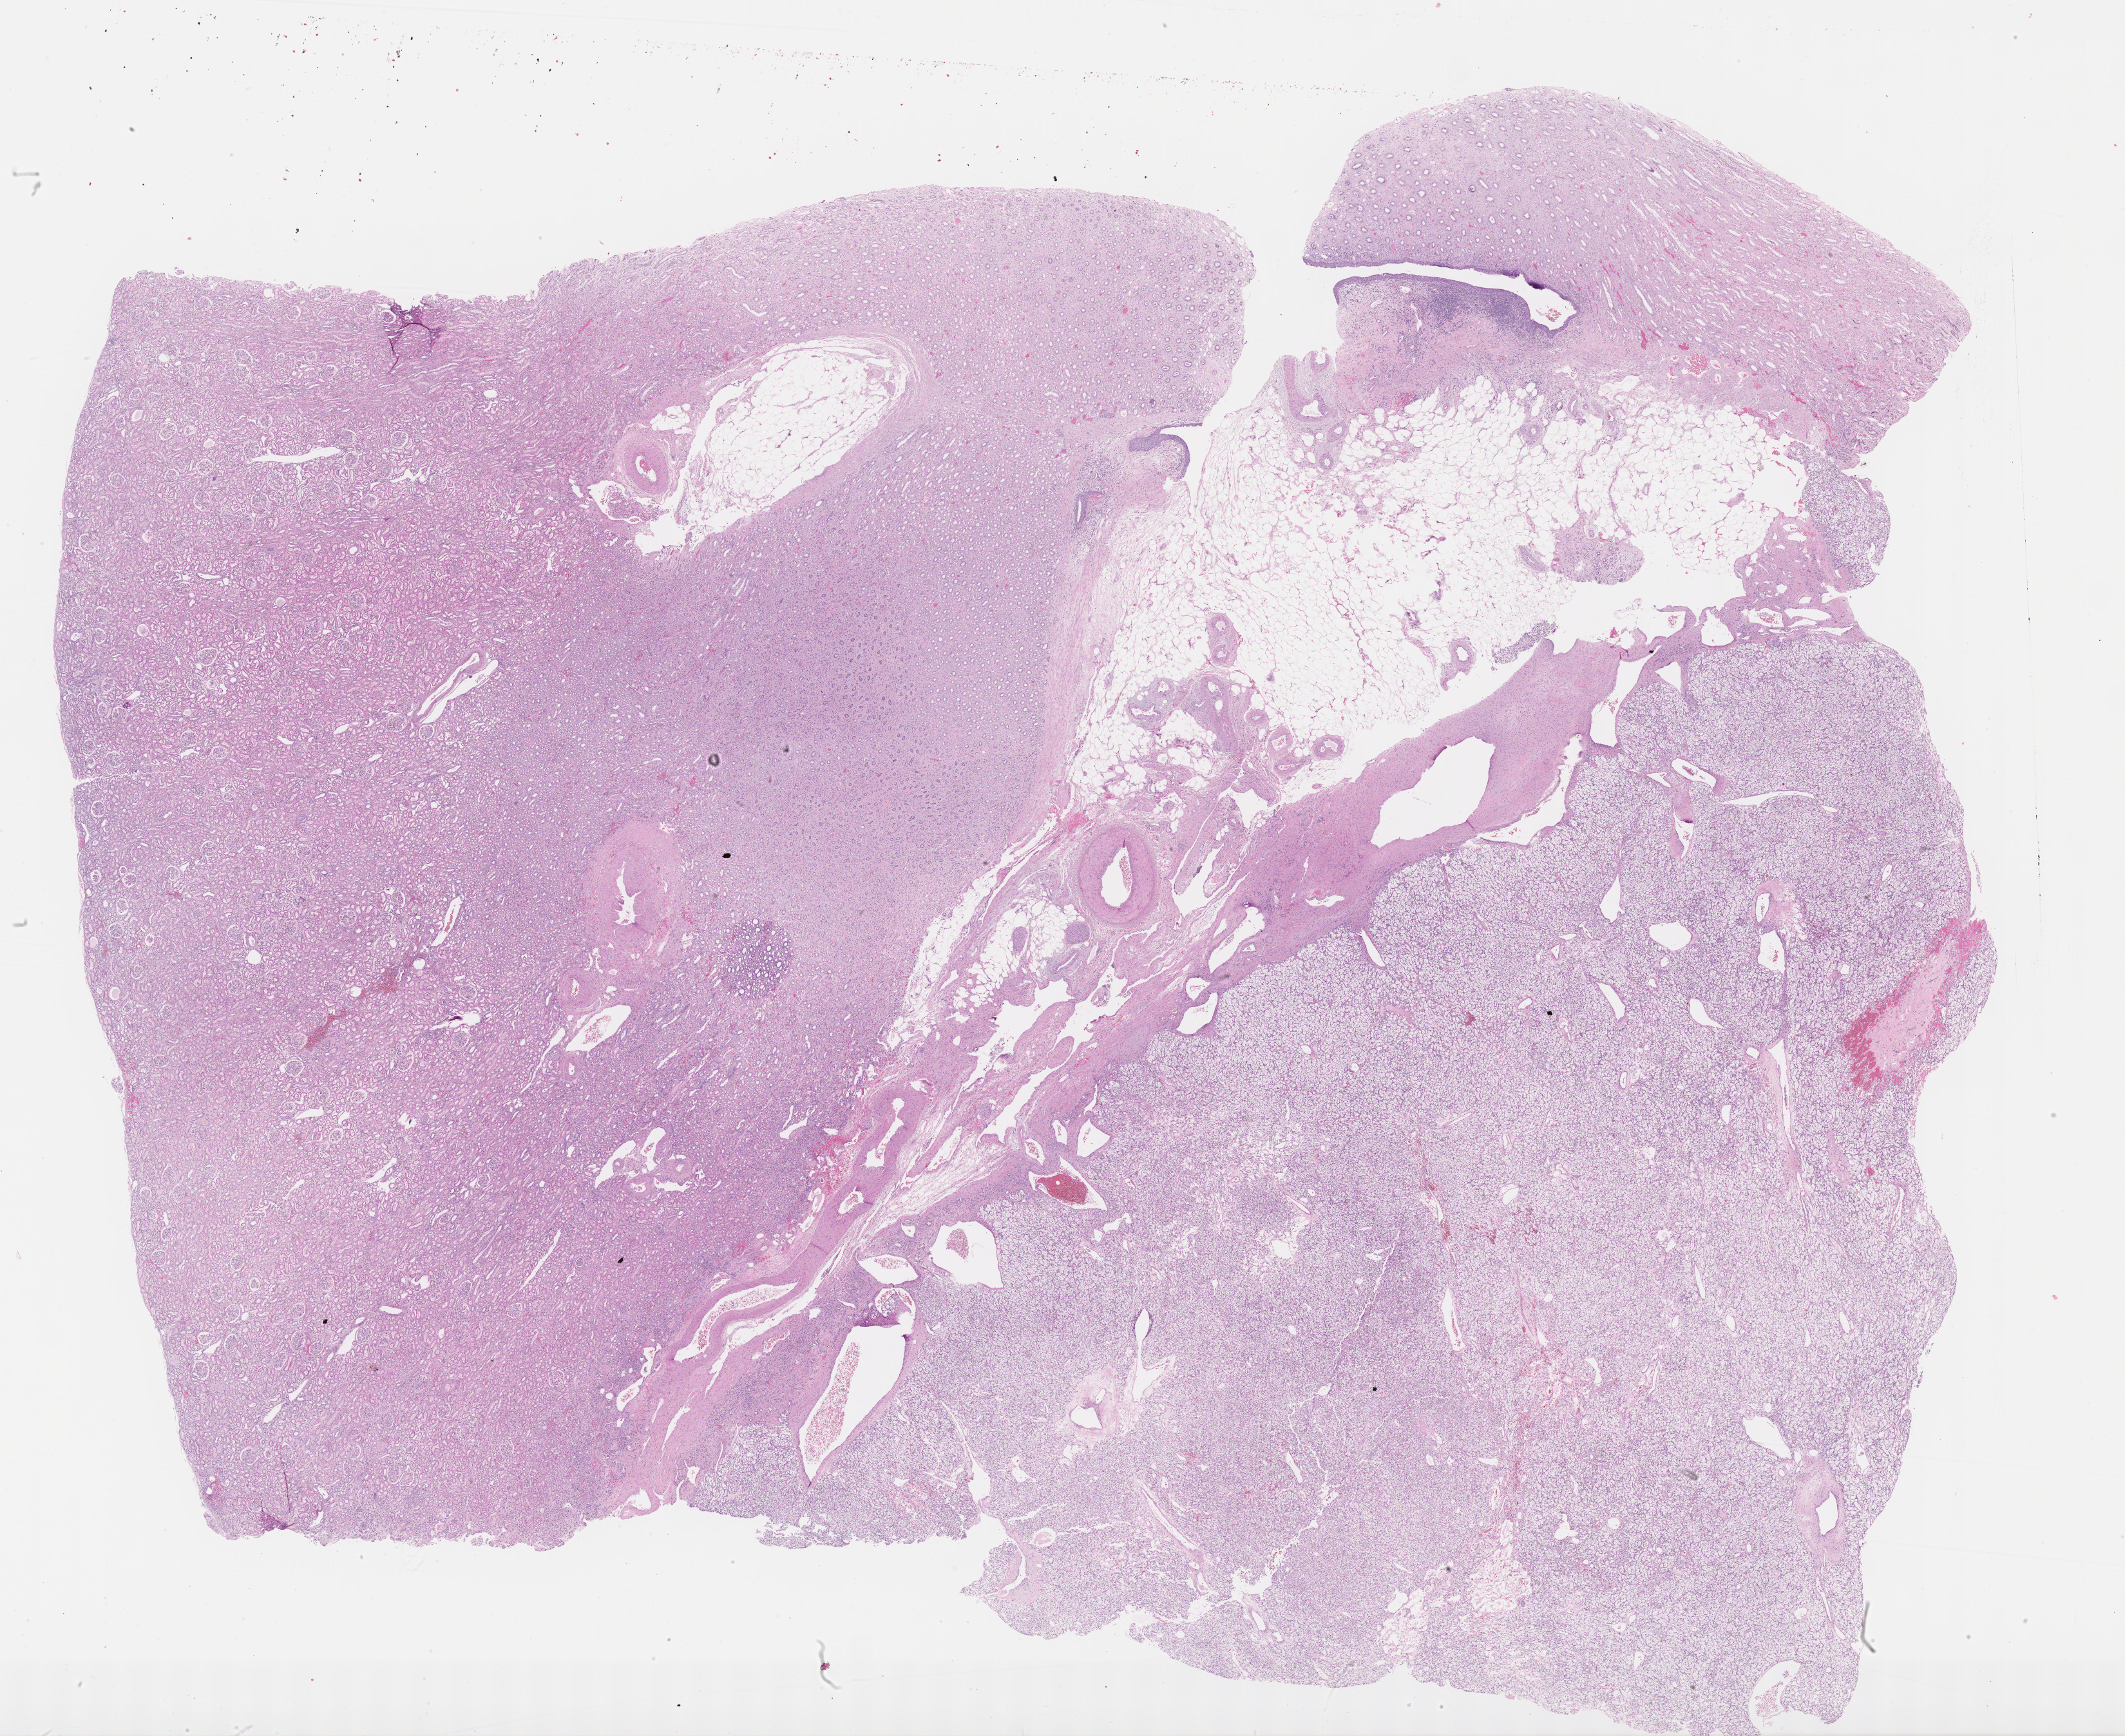
Whole-slide histology image, Hematoxylin and eosin (H&E) stained — shown as a low-resolution overview of the whole scanned area (about 26.7 x 21.8 mm, slide scanned at 40x). Formalin-fixed paraffin-embedded (FFPE) diagnostic section. Kidney, primary tumour sample. Female patient; age at initial diagnosis 58 years.
Histologic diagnosis: Clear cell adenocarcinoma, NOS.